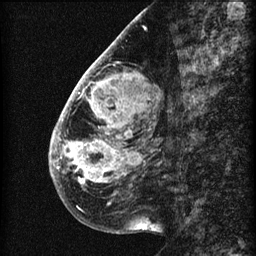
Breast MRI (dynamic contrast-enhanced), one sagittal slice; slice 22 of 60 in the series (ordered by position); 3 images stored at this slice position (order not interpretable as contrast timing); 1.5 T; TE 4.2 ms, TR 22.7 ms; 256 × 256 image matrix. Female patient, age 48 years. Case-level facts recorded for this patient, not image findings: setting: breast cancer imaged before/during neoadjuvant chemotherapy; receptor status: triple-negative.
Annotated regions visible in this slice (semi-automatic segmentation, software-assisted and operator-edited):
- analysis volume of interest (the breast-tissue region the enhancement analysis was run in; not a lesion): box from (x=50, y=30) to (x=173, y=207) px
- tumour enhancement mask (voxels above the 90 % enhancement threshold inside the analysis volume of interest): (x=50, y=55)–(x=135, y=190)